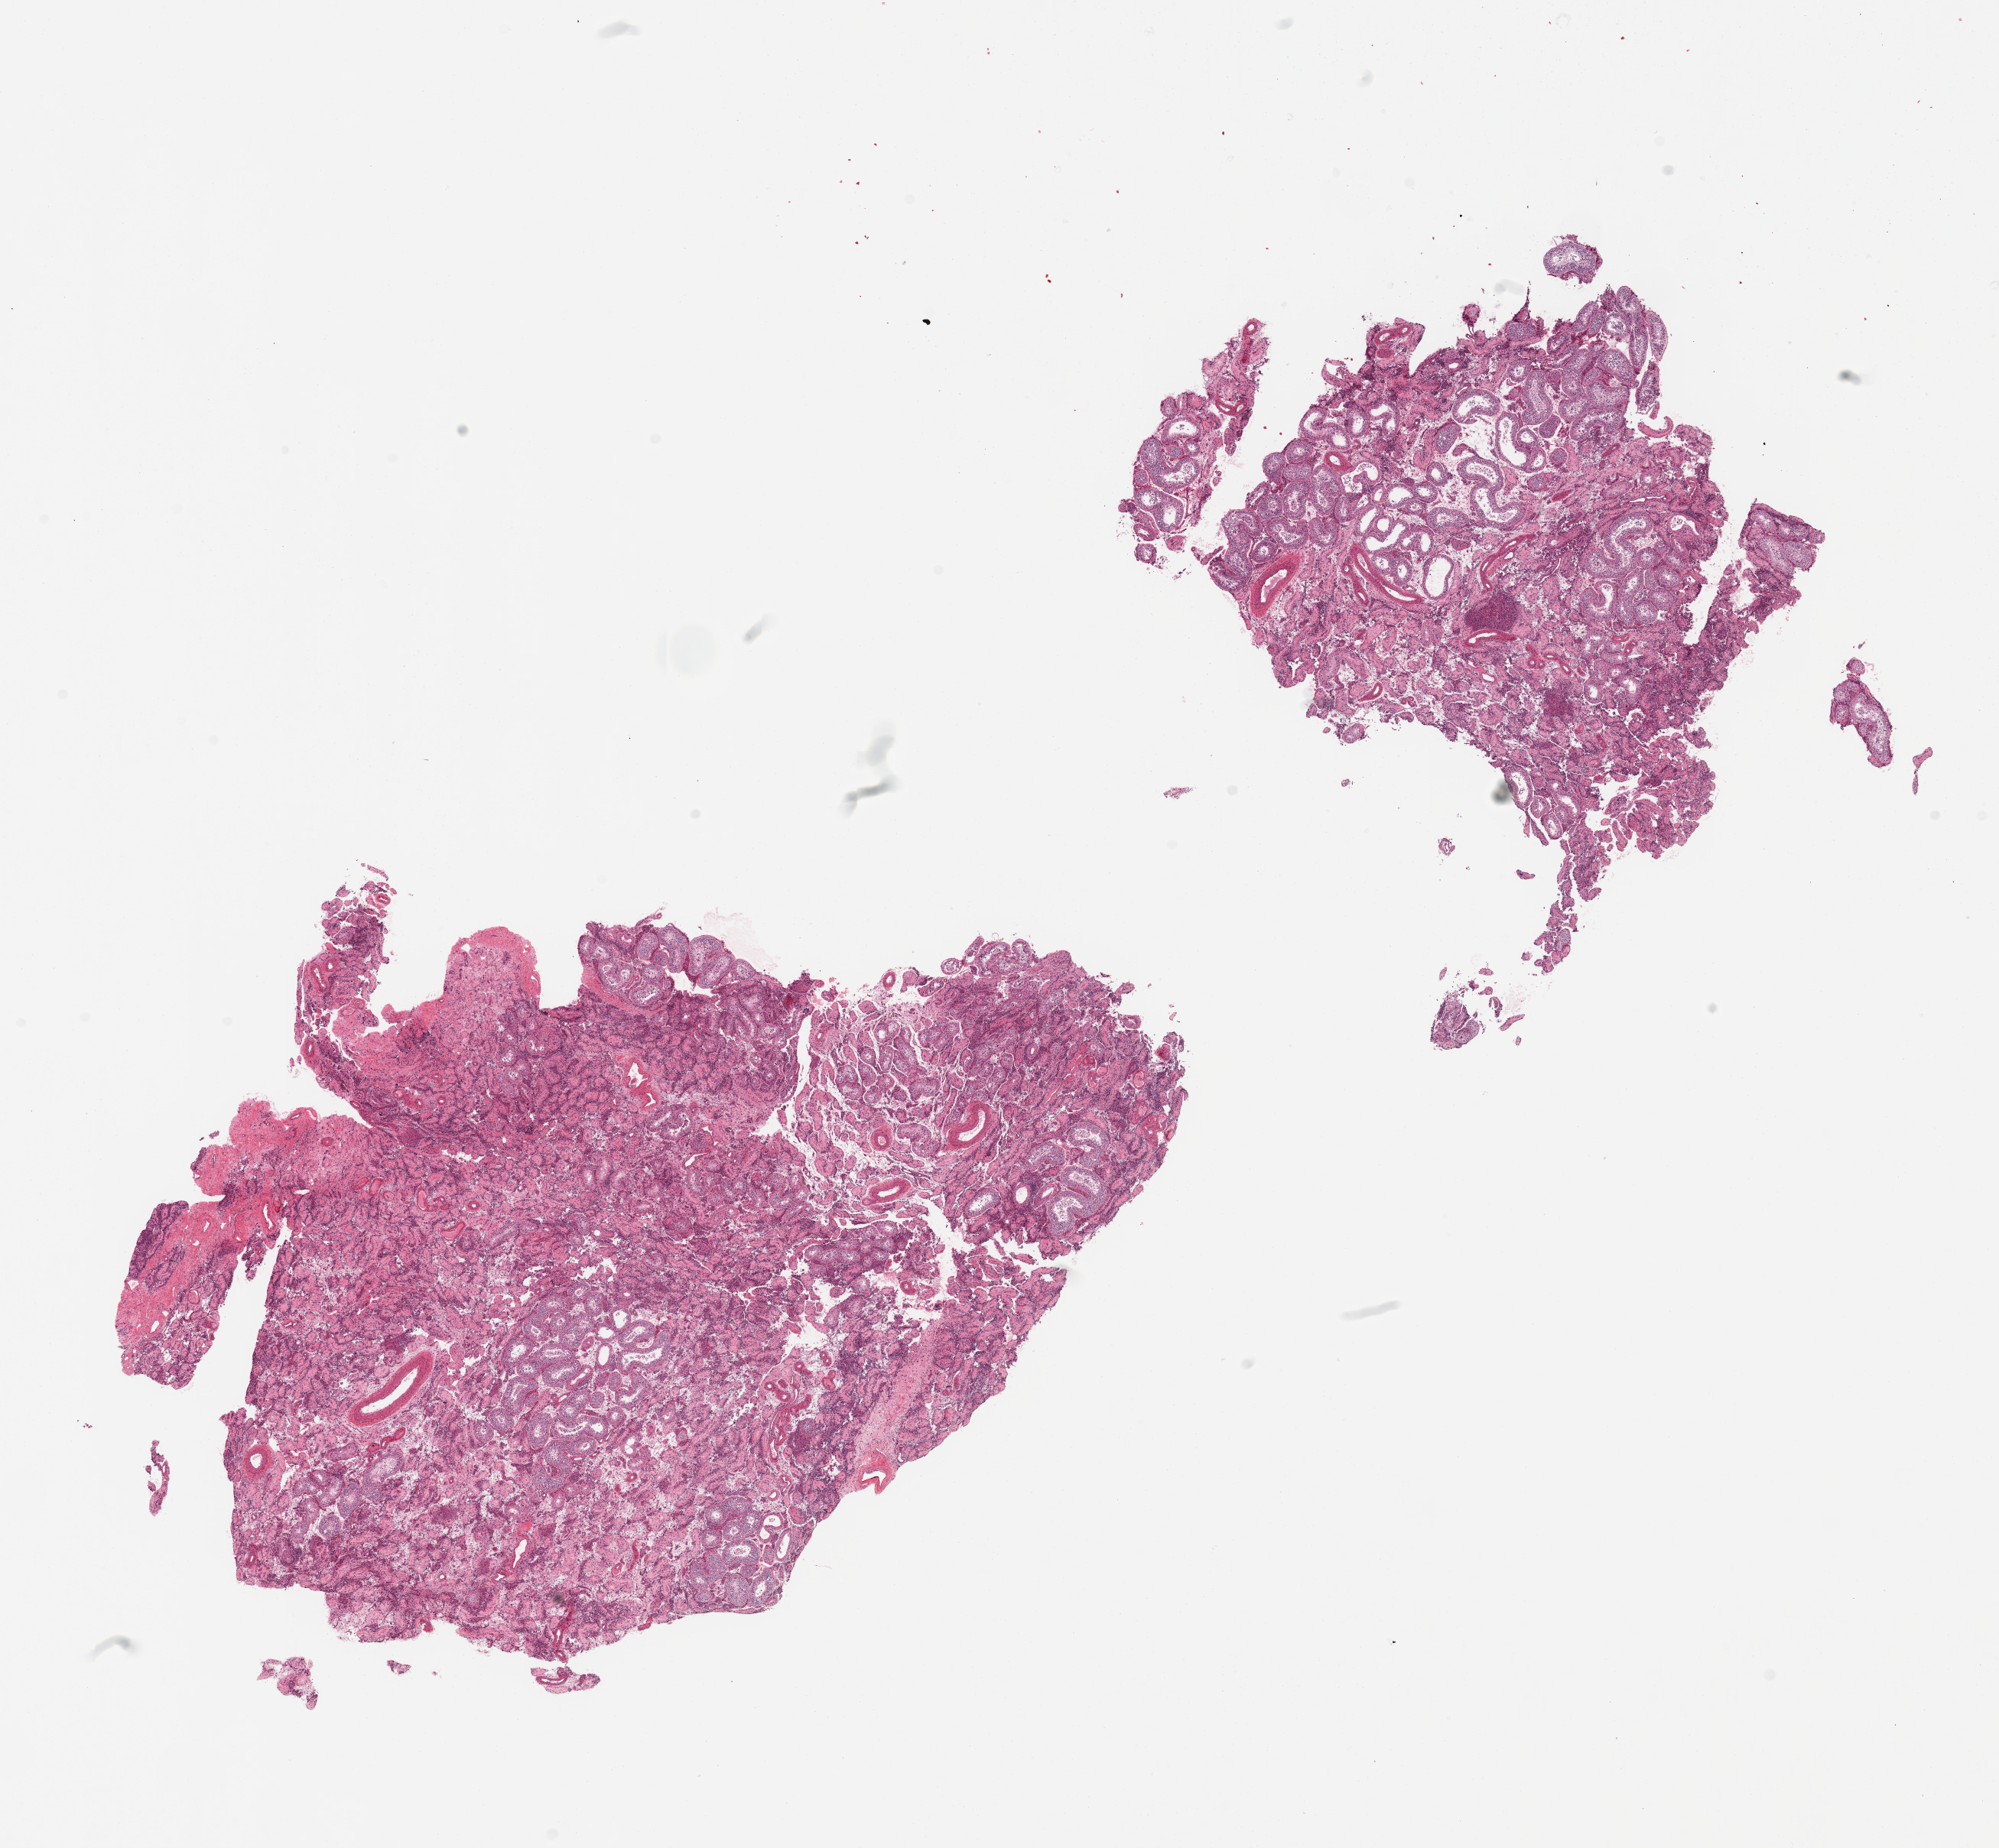
Hematoxylin and eosin (H&E) whole-slide image, whole scanned area (about 20.7 x 19.1 mm) shown as a low-resolution overview; PAXgene-fixed paraffin-embedded (PFPE) section; sampled site (target tissue): testis; donor tissue sample.
• pathologist's review note for this sample: 2 pieces; 70% tubules are fibrotic; Leydig cell hyperplasia; reduced spermatogenesis